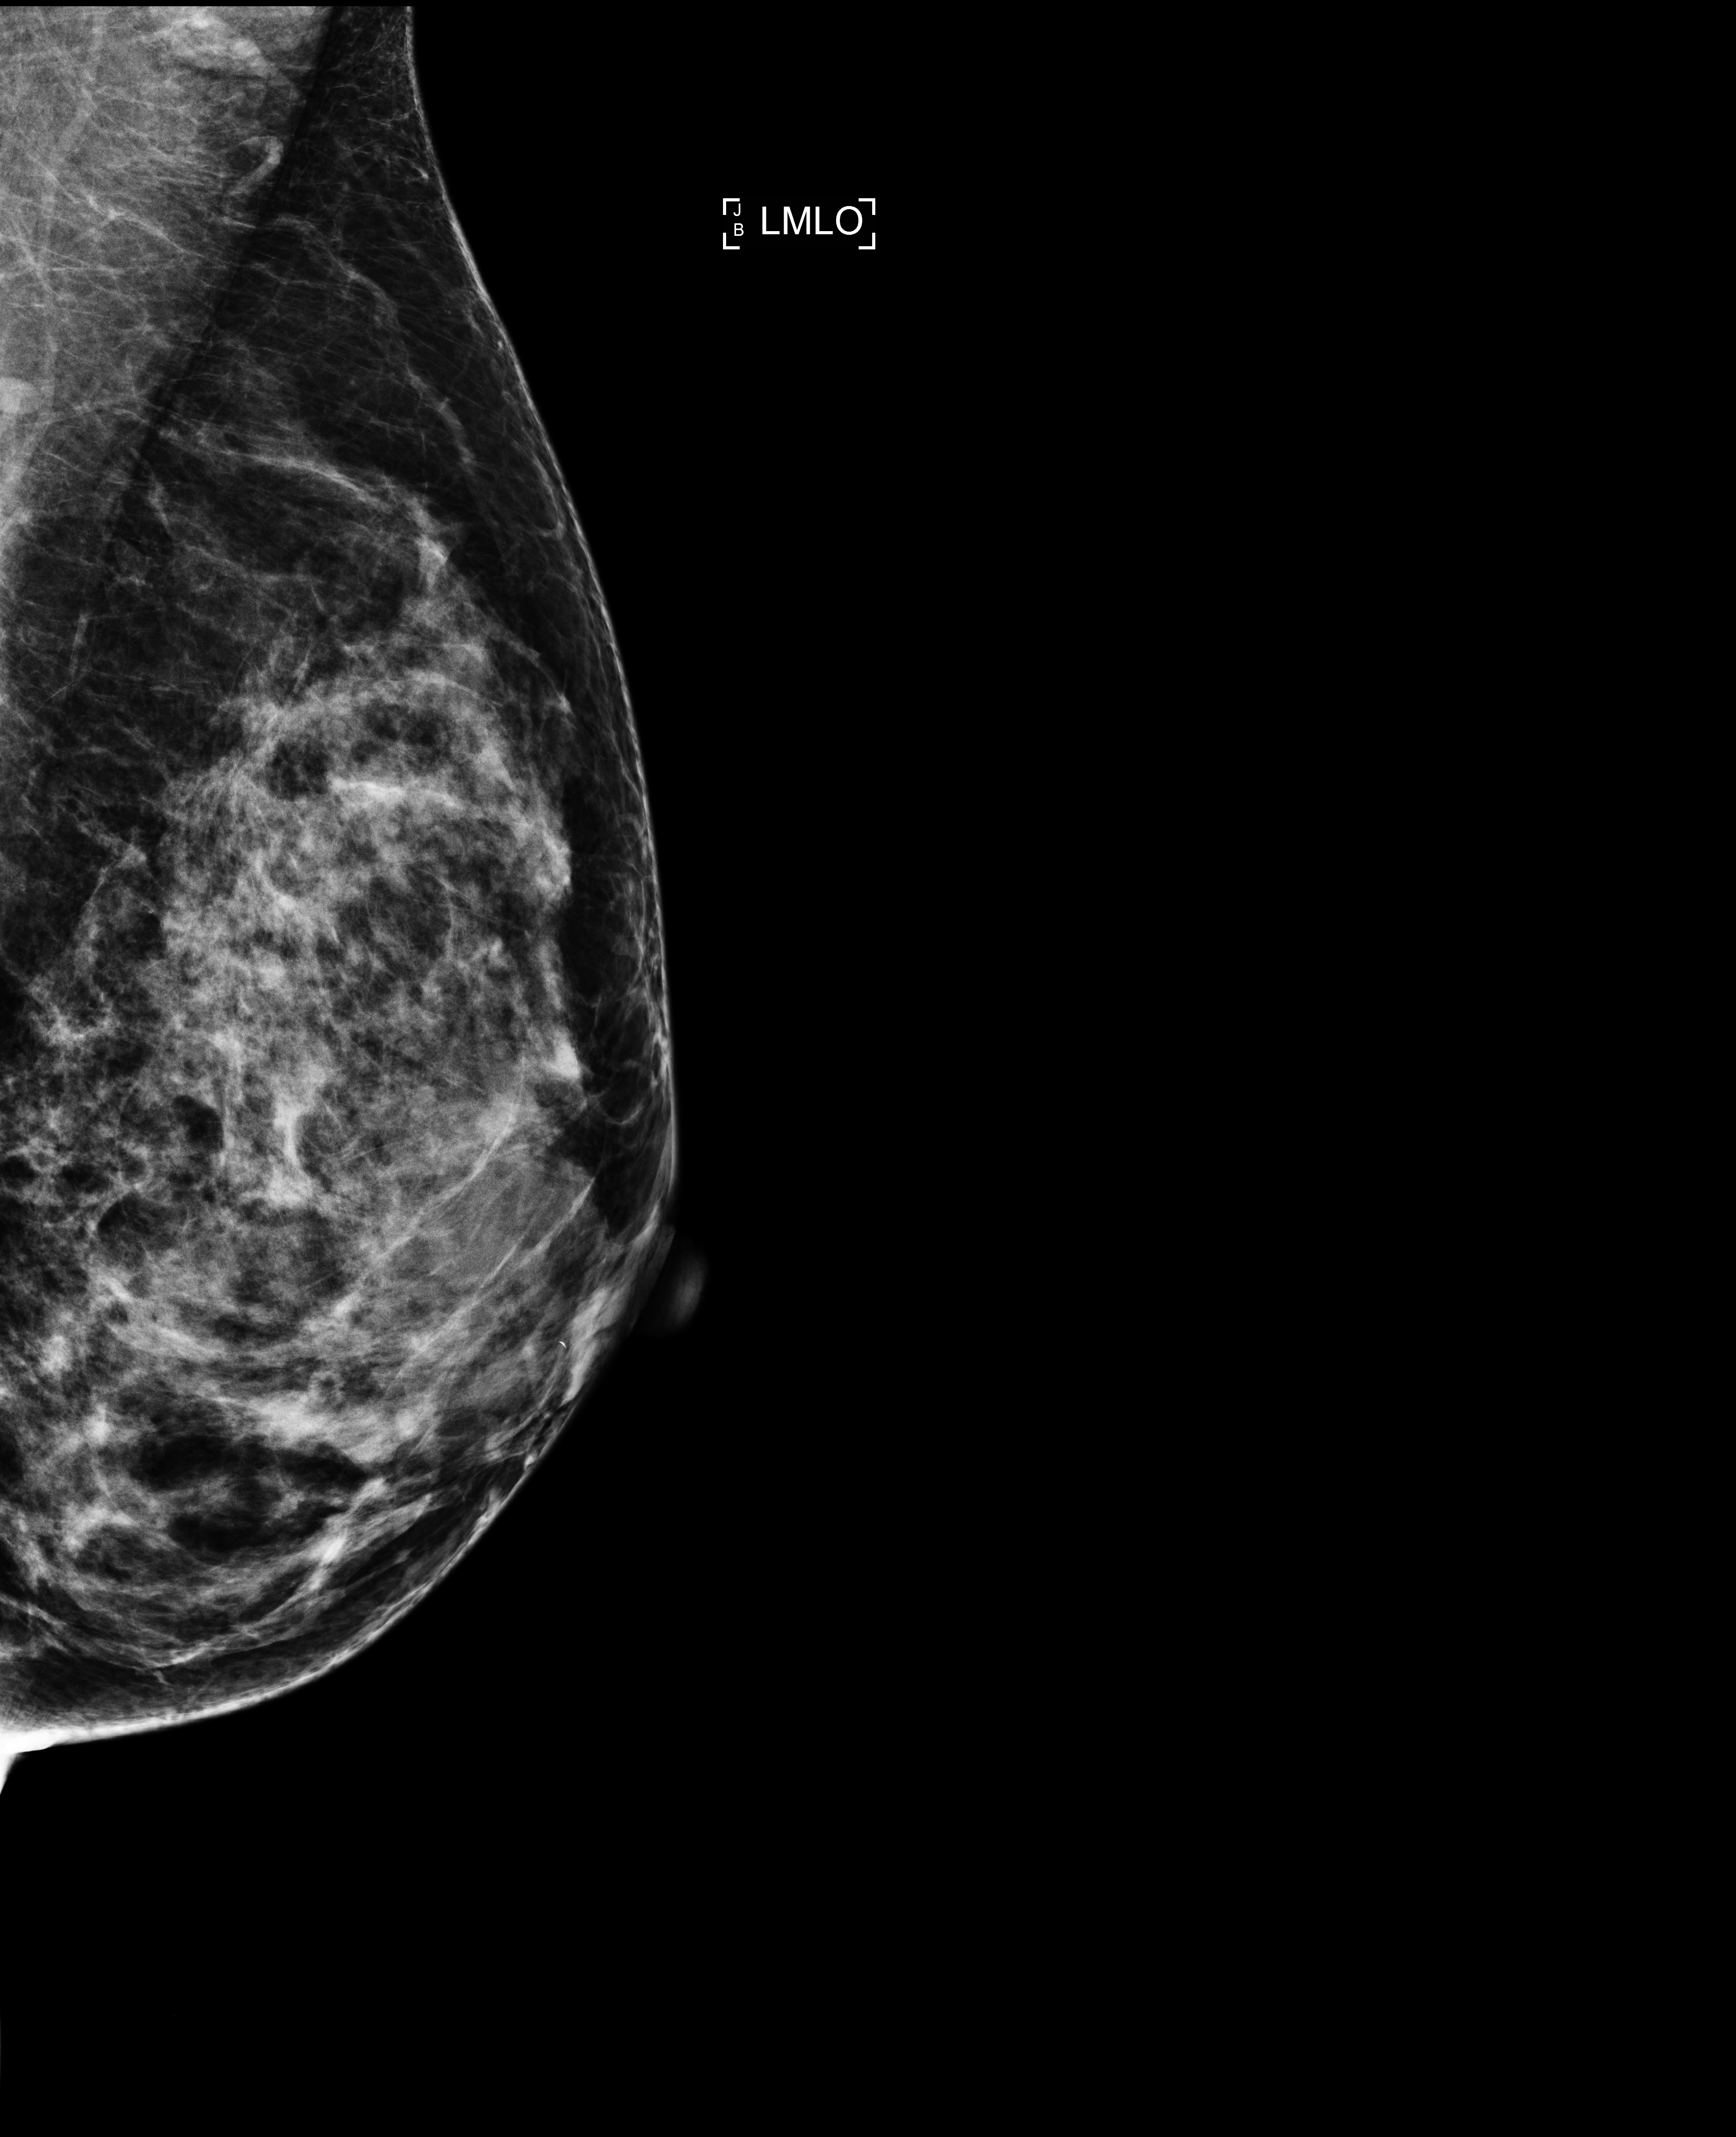
Annual screening mammography examination; compressed breast thickness 63 mm. Patient: female, 42 years.
Image type: full-field digital mammogram. Breast: left. Projection: medio-lateral oblique projection.